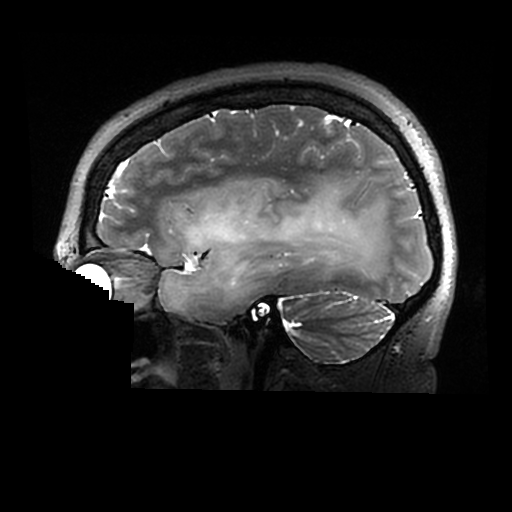
Brain MRI from a brain-tumour surgery series, one sagittal slice. Position 208 of 320 along the scan axis. 0.6 mm slice thickness. 512 × 512 image matrix, field of view 240 × 240 mm. From the clinical record (not read from this slice): histopathology: Astrocytoma; WHO grade: 2; IDH mutation: yes.
Outlined on this slice (outlined manually by an expert reader):
- tumour: bounding box <159,180,387,312> (left, top, right, bottom; pixels)